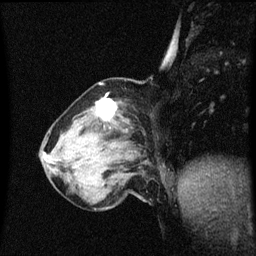
Breast MRI (dynamic contrast-enhanced), one sagittal slice; slice 17 of 60 in the series (ordered by position); dynamic contrast-enhanced series, image 2 of 3 at this slice position (ordered by acquisition); 1.5 T; TE 4.2 ms, TR 8.4 ms; 2 mm slice thickness; 256 × 256 image matrix, field of view 200 × 200 mm. Patient: female, 64 years. From the clinical record (not read from this slice): setting: breast cancer imaged before/during neoadjuvant chemotherapy; receptor status: HR-positive, HER2-negative.
Annotated regions visible in this slice (semi-automatically segmented with operator editing):
- analysis volume of interest (the breast-tissue region the enhancement analysis was run in; not a lesion): bounding box [x1, y1, x2, y2] px = [58, 96, 141, 167]
- tumour enhancement mask (voxels above the 70 % enhancement threshold inside the analysis volume of interest): [98, 100, 117, 119]